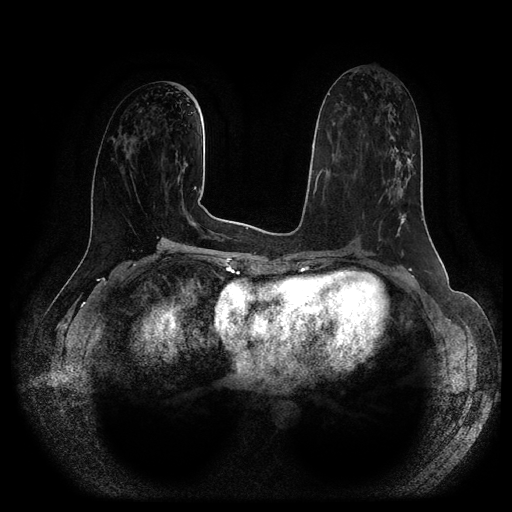
Breast MRI (dynamic contrast-enhanced, multi-phase), one axial slice; slice 49 of 116 in the series (ordered by position); dynamic contrast-enhanced series, time point 2 of 5 at this slice position (early post-contrast); 1.5 T; TE 2.6 ms, TR 5.2 ms; 2 mm slice thickness; 512 × 512 image matrix. Female patient, age 57 years.
Annotated regions visible in this slice (semi-automatically segmented with operator editing):
- breast lesion (labelled 'tumour' in the annotation; benign lesions carry a separate 'benign' label): bounding box (x1, y1, x2, y2) in pixels: (383, 132, 416, 200)